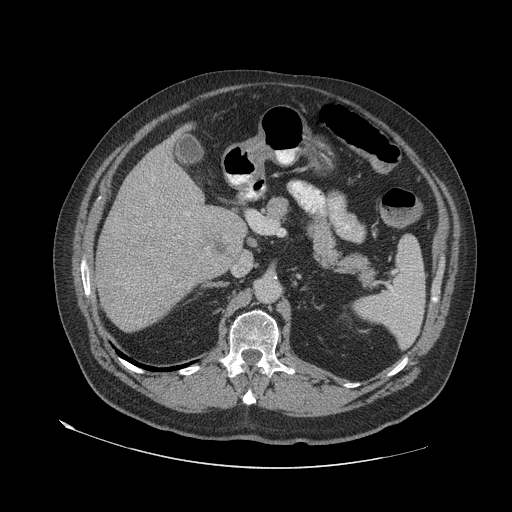
Contrast-enhanced abdominal CT (liver protocol), one axial slice. Slice 31 of 79 in the series (ordered by position). Reconstruction kernel STANDARD. Soft-tissue window (W 400 / L 40 HU). 512 × 512 image matrix. Case-level facts recorded for this patient, not image findings: diagnosis: hepatocellular carcinoma (patient treated with transarterial chemoembolisation; whether this scan precedes or follows treatment is not stated here); TNM stage (as recorded): Stage-IVA; Child-Pugh class: A; tumour nodularity: multinodular.
Annotated regions visible in this slice (semi-automatic segmentation, software-assisted and operator-edited):
- liver parenchyma outside the tumour (the mass and vessels are separate outlines, so this box may not span the whole liver): bounding box <96,130,246,330> (left, top, right, bottom; pixels)
- mass: <120,248,171,295>
- liver vessels: <179,213,190,237>